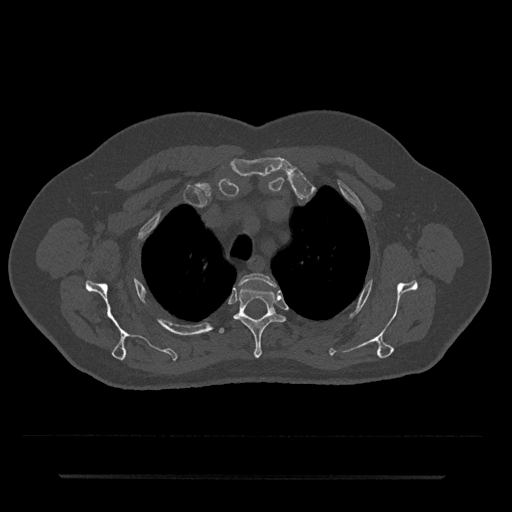
CT including the spine, one axial slice. Slice 568 of 797 in the series (ordered by position). 120 kVp. Bone window (W 1800 / L 400 HU). 0.5 mm slice thickness. 512 × 512 image matrix. Patient: male, 69 years. Case-level facts recorded for this patient, not image findings: primary cancer: prostate.
Annotated regions visible in this slice (semi-automatic segmentation, software-assisted and operator-edited):
- T2 vertebra: bounding box (x1, y1, x2, y2) in pixels: (240, 273, 276, 287)
- T3 vertebra: (234, 287, 285, 358)
- T4 vertebra: (219, 328, 225, 334)